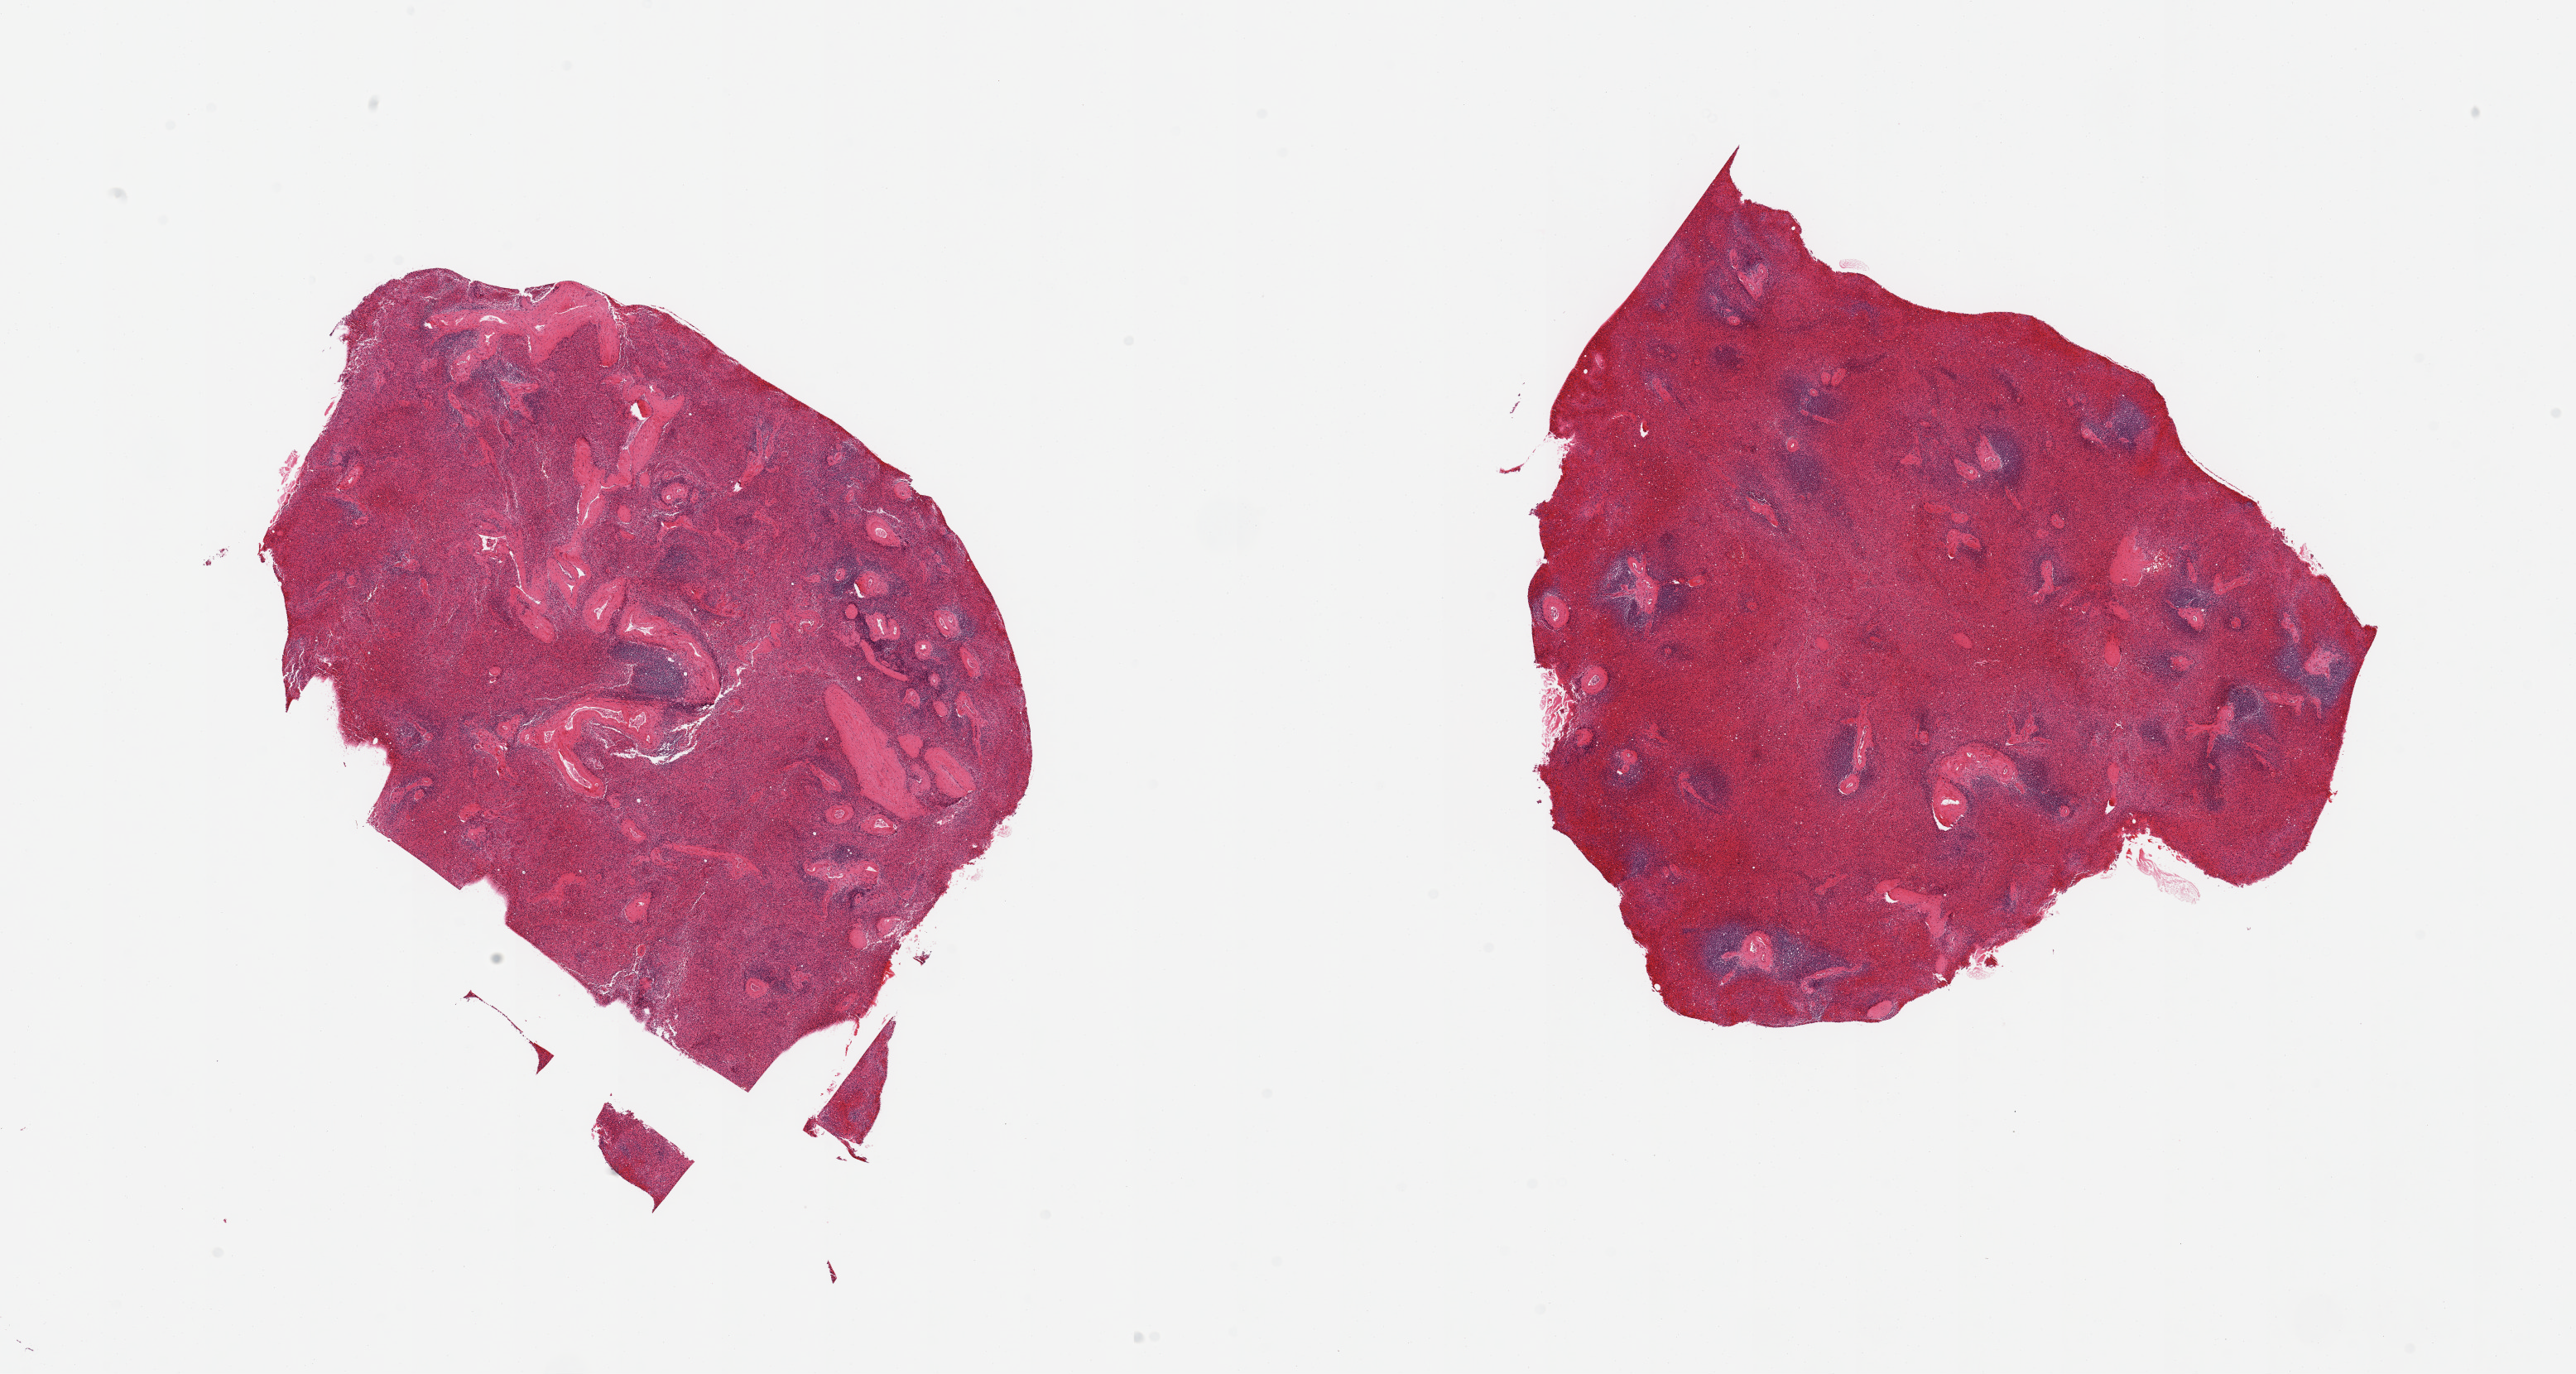
H&E whole-slide image, brightfield, low-resolution overview of the scanned area, about 24.6 x 13.1 mm (slide scanned at 20x); PAXgene-fixed paraffin-embedded (PFPE) section; target tissue: spleen; donor tissue sample. Male donor.
• review note (as recorded): 2 pieces; moderately congested